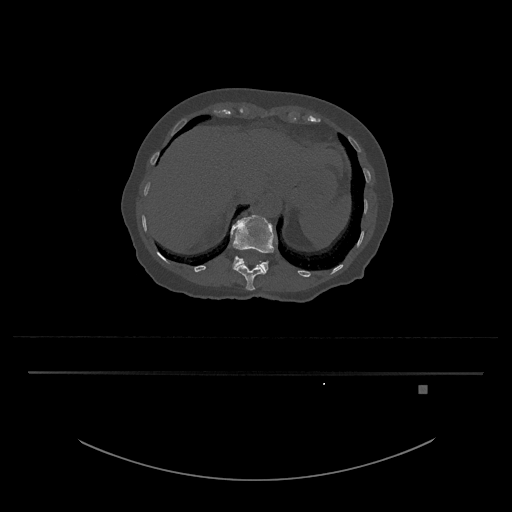
CT including the spine, one axial slice. Slice 585 of 797 in the series (ordered by position). 120 kVp. Bone window (W 1800 / L 400 HU). 512 × 512 image matrix, field of view 500 × 500 mm. Patient: female, 57 years. Case-level facts recorded for this patient, not image findings: primary cancer: cervical.
Annotated regions visible in this slice (semi-automatic segmentation, software-assisted and operator-edited):
- L1 vertebra: bounding box [x1, y1, x2, y2] px = [231, 215, 278, 273]
- T12 vertebra: [235, 262, 266, 290]